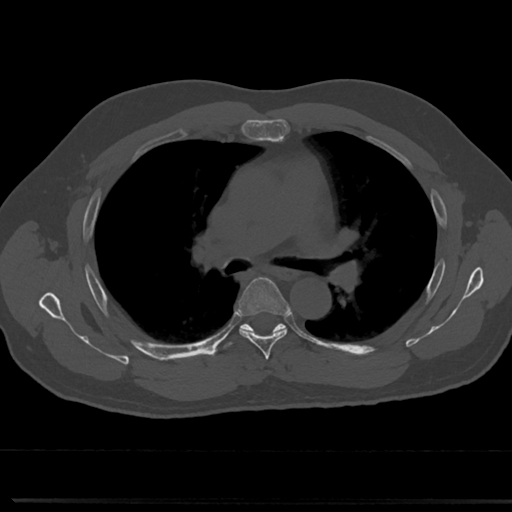
CT including the spine, one axial slice. Slice 486 of 817 in the series (ordered by position). Reconstruction kernel Br40s/3. 120 kVp. Bone window (W 1800 / L 400 HU). 0.5 mm slice thickness. 512 × 512 image matrix. Patient: male, 61 years. From the clinical record (not read from this slice): primary cancer: prostate.
Structures marked on this image (semi-automatically segmented with operator editing):
- T4 vertebra: bounding box <265,366,273,374> (left, top, right, bottom; pixels)
- T5 vertebra: <235,278,290,353>
- T6 vertebra: <242,327,284,332>